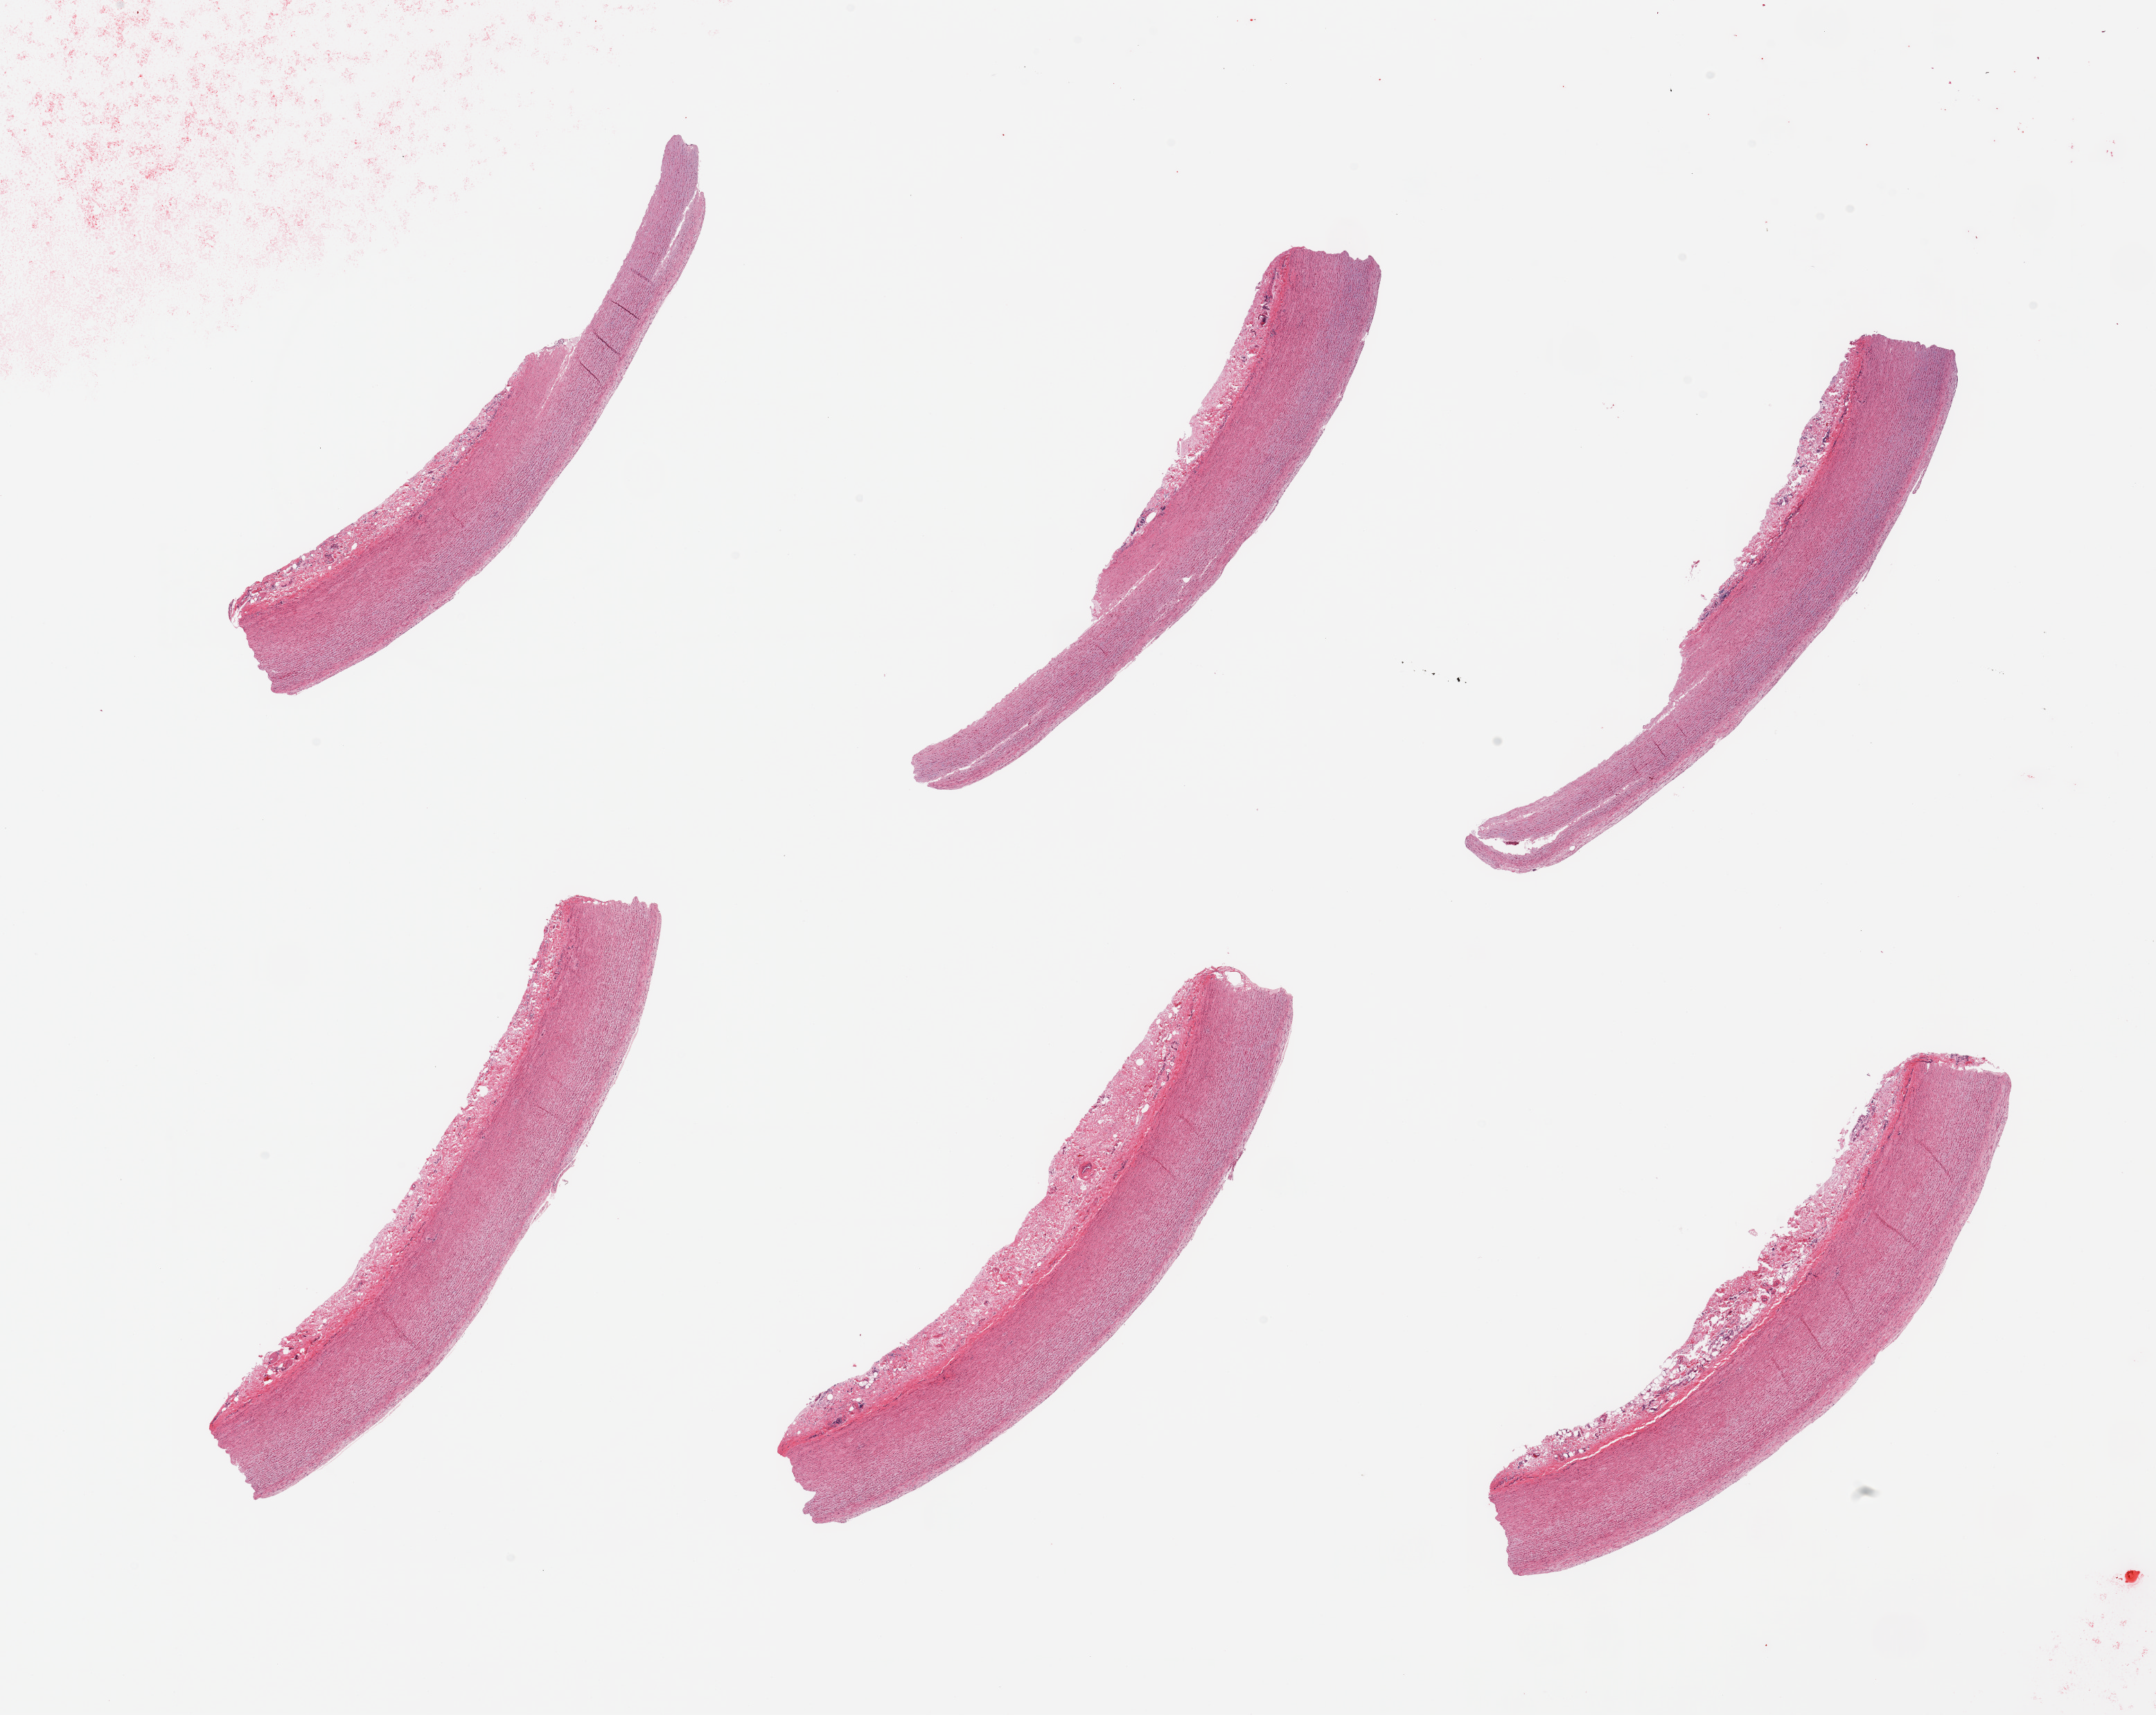
Haematoxylin and eosin whole-slide image, brightfield — whole scanned area (about 24.6 x 19.6 mm, from a 20x scan) shown as a low-resolution overview. PAXgene-fixed paraffin-embedded (PFPE) section. Section of aorta (target tissue). Tissue donor sample. Donor sex: male.
• pathologist's review note for this sample: 6 pieces